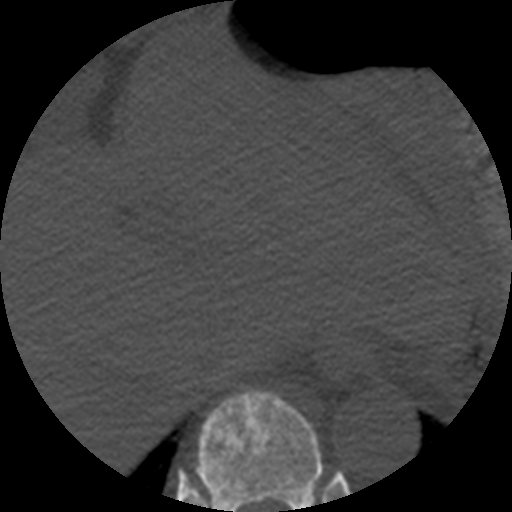
CT including the spine, one axial slice; slice 273 of 508 in the series (ordered by position); bone window (W 1800 / L 400 HU); 1.25 mm slice thickness; 512 × 512 image matrix, field of view 160 × 160 mm. Patient age 57 years. Case-level facts recorded for this patient, not image findings: primary cancer: prostate.
Structures marked on this image (semi-automatically segmented with operator editing):
- T10 vertebra: bounding box [x1, y1, x2, y2] px = [197, 388, 322, 512]